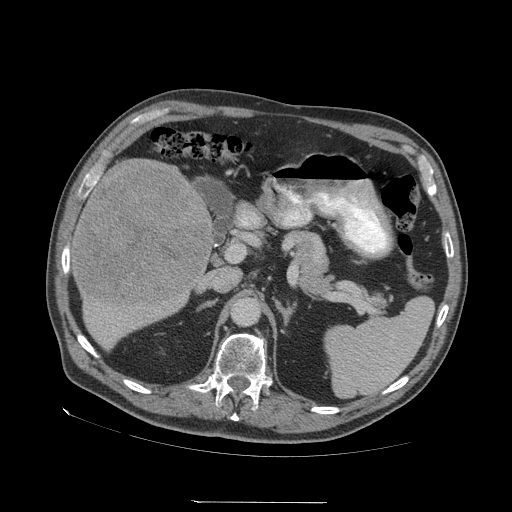
Contrast-enhanced abdominal CT (liver protocol), one axial slice; soft-tissue window (W 400 / L 40 HU); 2.5 mm slice thickness; 512 × 512 image matrix, field of view 460 × 460 mm. Case-level facts recorded for this patient, not image findings: diagnosis: hepatocellular carcinoma (patient treated with transarterial chemoembolisation; whether this scan precedes or follows treatment is not stated here); TNM stage (as recorded): Stage-I; Child-Pugh class: A; tumour nodularity: uninodular.
Annotated regions visible in this slice (semi-automatic segmentation, software-assisted and operator-edited):
- liver parenchyma outside the tumour (the mass and vessels are separate outlines, so this box may not span the whole liver): bounding box (x1, y1, x2, y2) in pixels: (68, 158, 217, 348)
- mass: (72, 159, 210, 303)